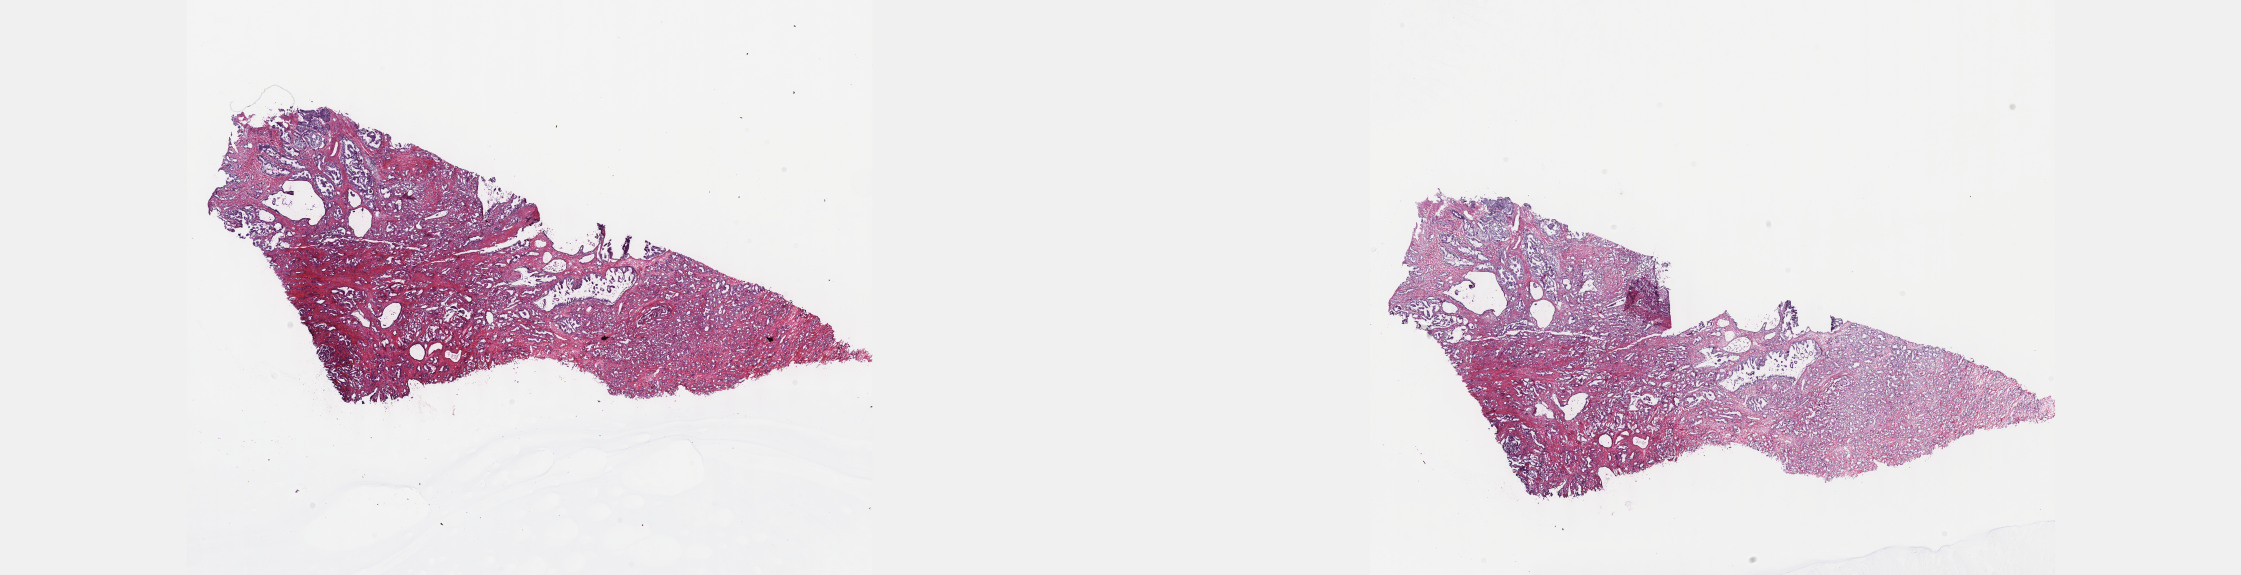
Digitized Hematoxylin and eosin (H&E) stained tissue section (whole slide) — low-resolution overview of the scanned area, about 36.2 x 9.3 mm (slide scanned at 40x); frozen section from the top of the tissue portion; primary tumour sample from the prostate. Male, age 69 years at initial diagnosis. Gleason score: 7 (4+3). Slide review estimates, as recorded: tumour cells 70%, tumour nuclei 80%, normal cells 10%, stromal cells 20%, necrosis 0%. Infiltration values recorded for this section: lymphocyte infiltration 0%, monocyte infiltration 0%, neutrophil infiltration 0%.
• histologic diagnosis: Adenocarcinoma, NOS
• lymph nodes positive (case pathology): 0 of 21 examined